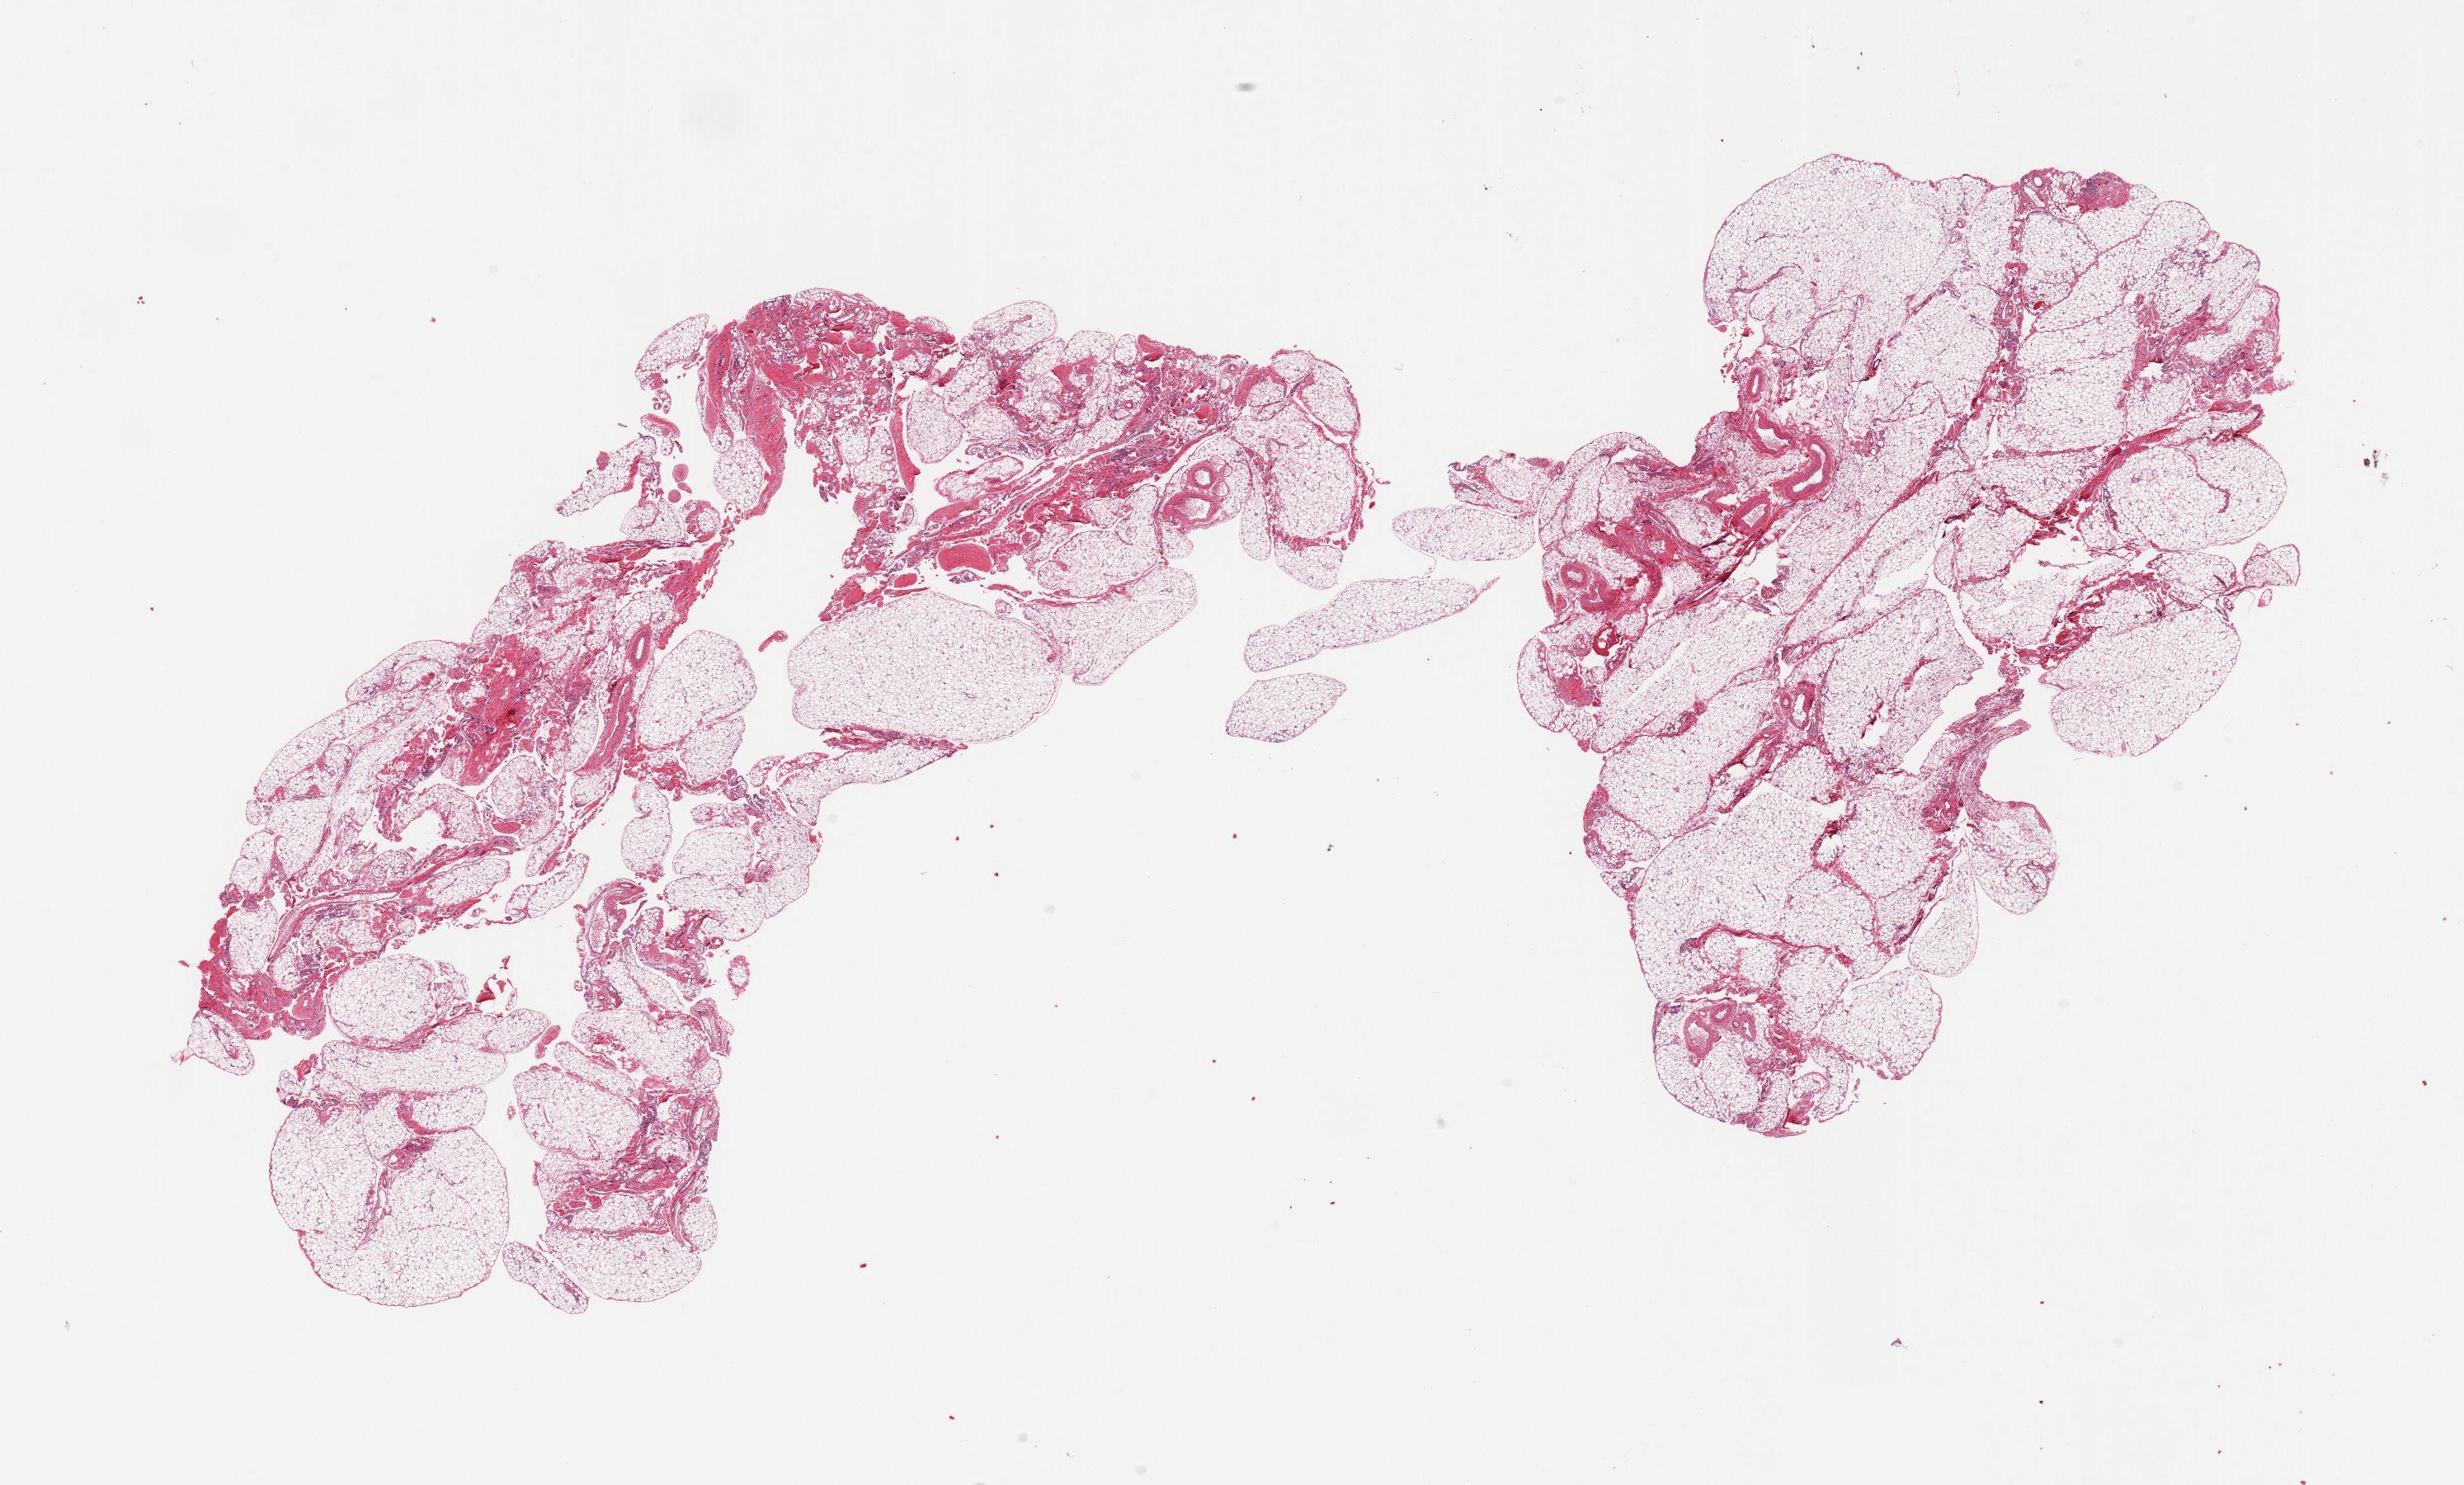
Haematoxylin and eosin whole-slide image — shown as a low-resolution overview of the whole scanned area (about 23.6 x 14.2 mm). PAXgene-fixed, paraffin-embedded tissue. Sampled site (target tissue): omentum. Donor tissue sample. Male donor.
Review note (as recorded): 2 pieces; lobulated fat with up to 30% vessels/fibrous tissue, scattered inflammatory cells.